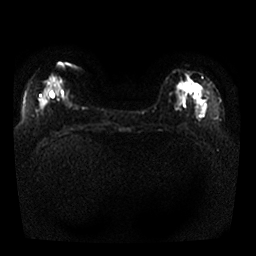
Breast MRI, one axial slice; position 10 of 25 along the scan axis; diffusion-weighted series; image 2 of 4 stored at this slice position (different b-values; order by instance number); 1.5 T; 256 × 256 image matrix. Female patient.
Structures marked on this image (expert manual segmentation):
- tumour on diffusion-weighted imaging: bounding box (x1, y1, x2, y2) in pixels: (178, 80, 197, 93)